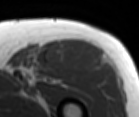
MRI of an extremity soft-tissue mass, one axial slice; slice 71 of 86 in the series (ordered by position); MR volume resampled by the dataset authors to the PET/CT grid (not the native acquisition matrix); 139 × 117 image matrix, field of view 136 × 114 mm. Male patient. Case-level facts recorded for this patient, not image findings: histological type: extraskeletal osteosarcoma; grade: high; site of the primary tumour: thigh.
Structures marked on this image (expert contour drawn on MRI and transferred to this co-registered scan by the dataset authors):
- gross tumour volume (mass): box from (x=45, y=41) to (x=103, y=74) px